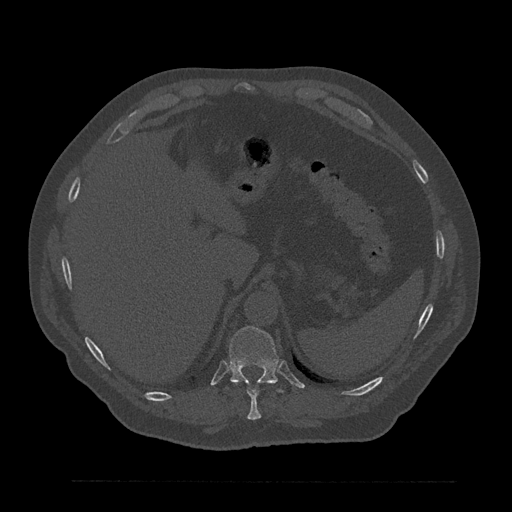
CT including the spine, one axial slice; slice 317 of 797 in the series (ordered by position); 120 kVp; bone window (W 1800 / L 400 HU); 0.5 mm slice thickness; 512 × 512 image matrix, field of view 430 × 430 mm. Male patient, age 61 years. Case-level facts recorded for this patient, not image findings: primary cancer: prostate.
Structures marked on this image (semi-automatic segmentation, software-assisted and operator-edited):
- T10 vertebra: bounding box <231,381,261,420> (left, top, right, bottom; pixels)
- T11 vertebra: <229,326,284,393>